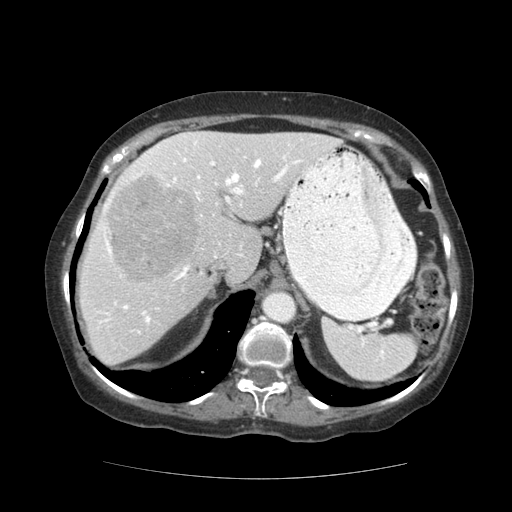
Contrast-enhanced abdominal CT (liver protocol), one axial slice. Position 84 of 111 along the scan axis. Soft-tissue window (W 400 / L 40 HU). 2.5 mm slice thickness. 512 × 512 image matrix, field of view 360 × 360 mm. Case-level facts recorded for this patient, not image findings: diagnosis: hepatocellular carcinoma (patient treated with transarterial chemoembolisation; whether this scan precedes or follows treatment is not stated here); TNM stage (as recorded): Stage-I; Child-Pugh class: A; tumour nodularity: uninodular.
Outlined on this slice (semi-automatic segmentation, software-assisted and operator-edited):
- liver parenchyma outside the tumour (the mass and vessels are separate outlines, so this box may not span the whole liver): bounding box <80,130,338,364> (left, top, right, bottom; pixels)
- mass: <106,177,200,280>
- liver vessels: <98,135,325,333>